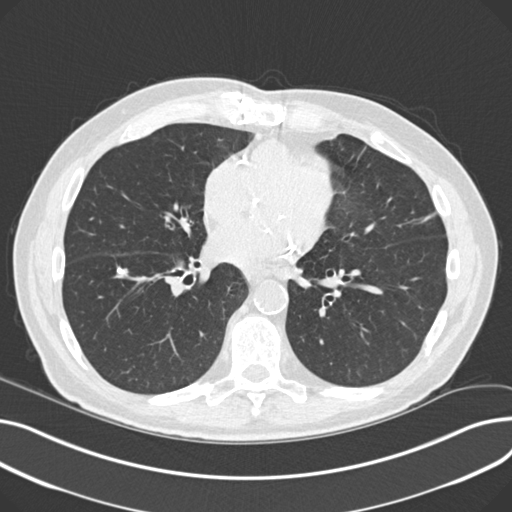
Low-dose screening chest CT, one axial slice; slice 96 of 230 in the series (ordered by position); reconstruction kernel B30f; 120 kVp; lung window (W 1500 / L -600 HU); 2 mm slice thickness; 512 × 512 image matrix, field of view 372 × 372 mm.
Annotated regions visible in this slice (outlined manually by an expert reader):
- lesion 2 (tumor, lower lobe of right lung): bounding box (x1, y1, x2, y2) in pixels: (115, 268, 128, 278)